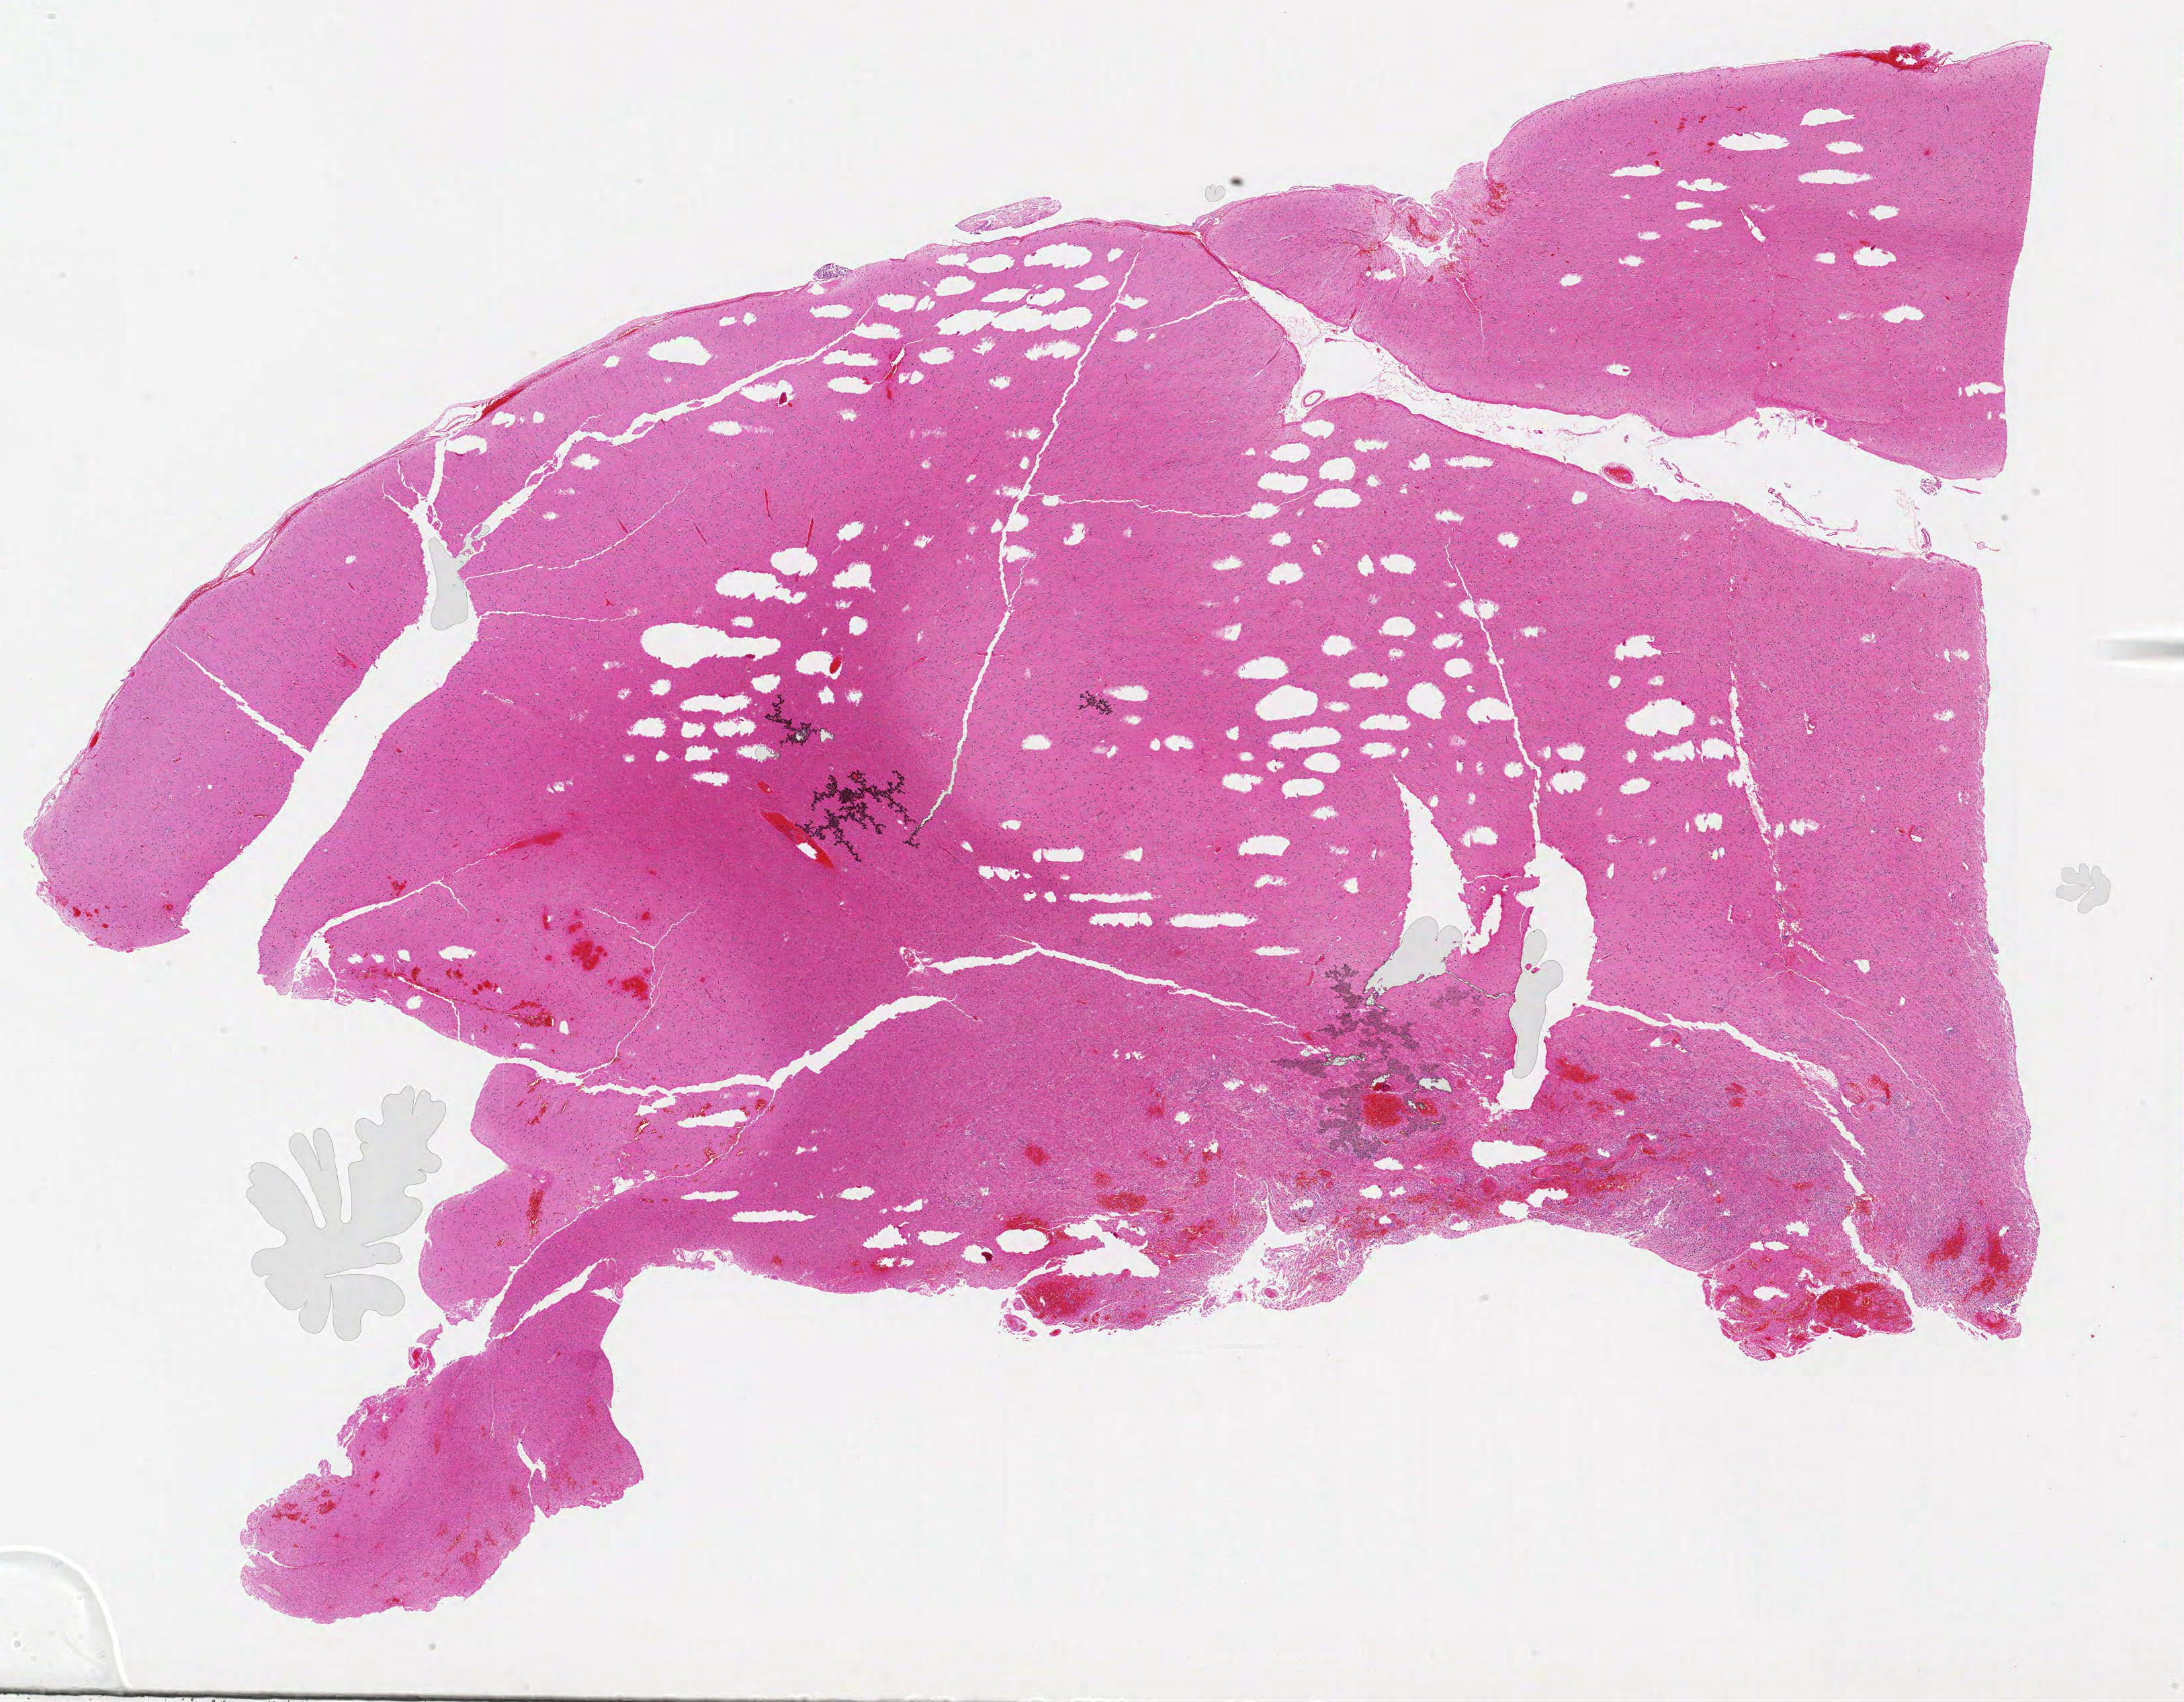
Whole-slide histology image, H&E-stained — a low-resolution overview of the entire scanned area, about 26.0 x 20.2 mm, formalin-fixed paraffin-embedded (FFPE) diagnostic section, brain, primary tumour sample. Male, age 58 years at initial diagnosis.
Diagnosis: Glioblastoma.